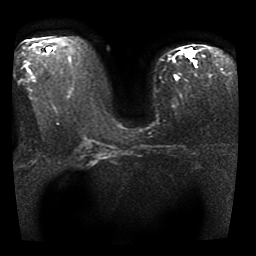
Breast MRI, one axial slice. Position 18 of 41 along the scan axis. Diffusion-weighted series; image 2 of 4 stored at this slice position (different b-values; order by instance number). 1.5 T. 5 mm slice thickness. 256 × 256 image matrix, field of view 330 × 330 mm. Female patient.
Annotated regions visible in this slice (outlined manually by an expert reader):
- tumour on diffusion-weighted imaging: bounding box <184,49,191,57> (left, top, right, bottom; pixels)